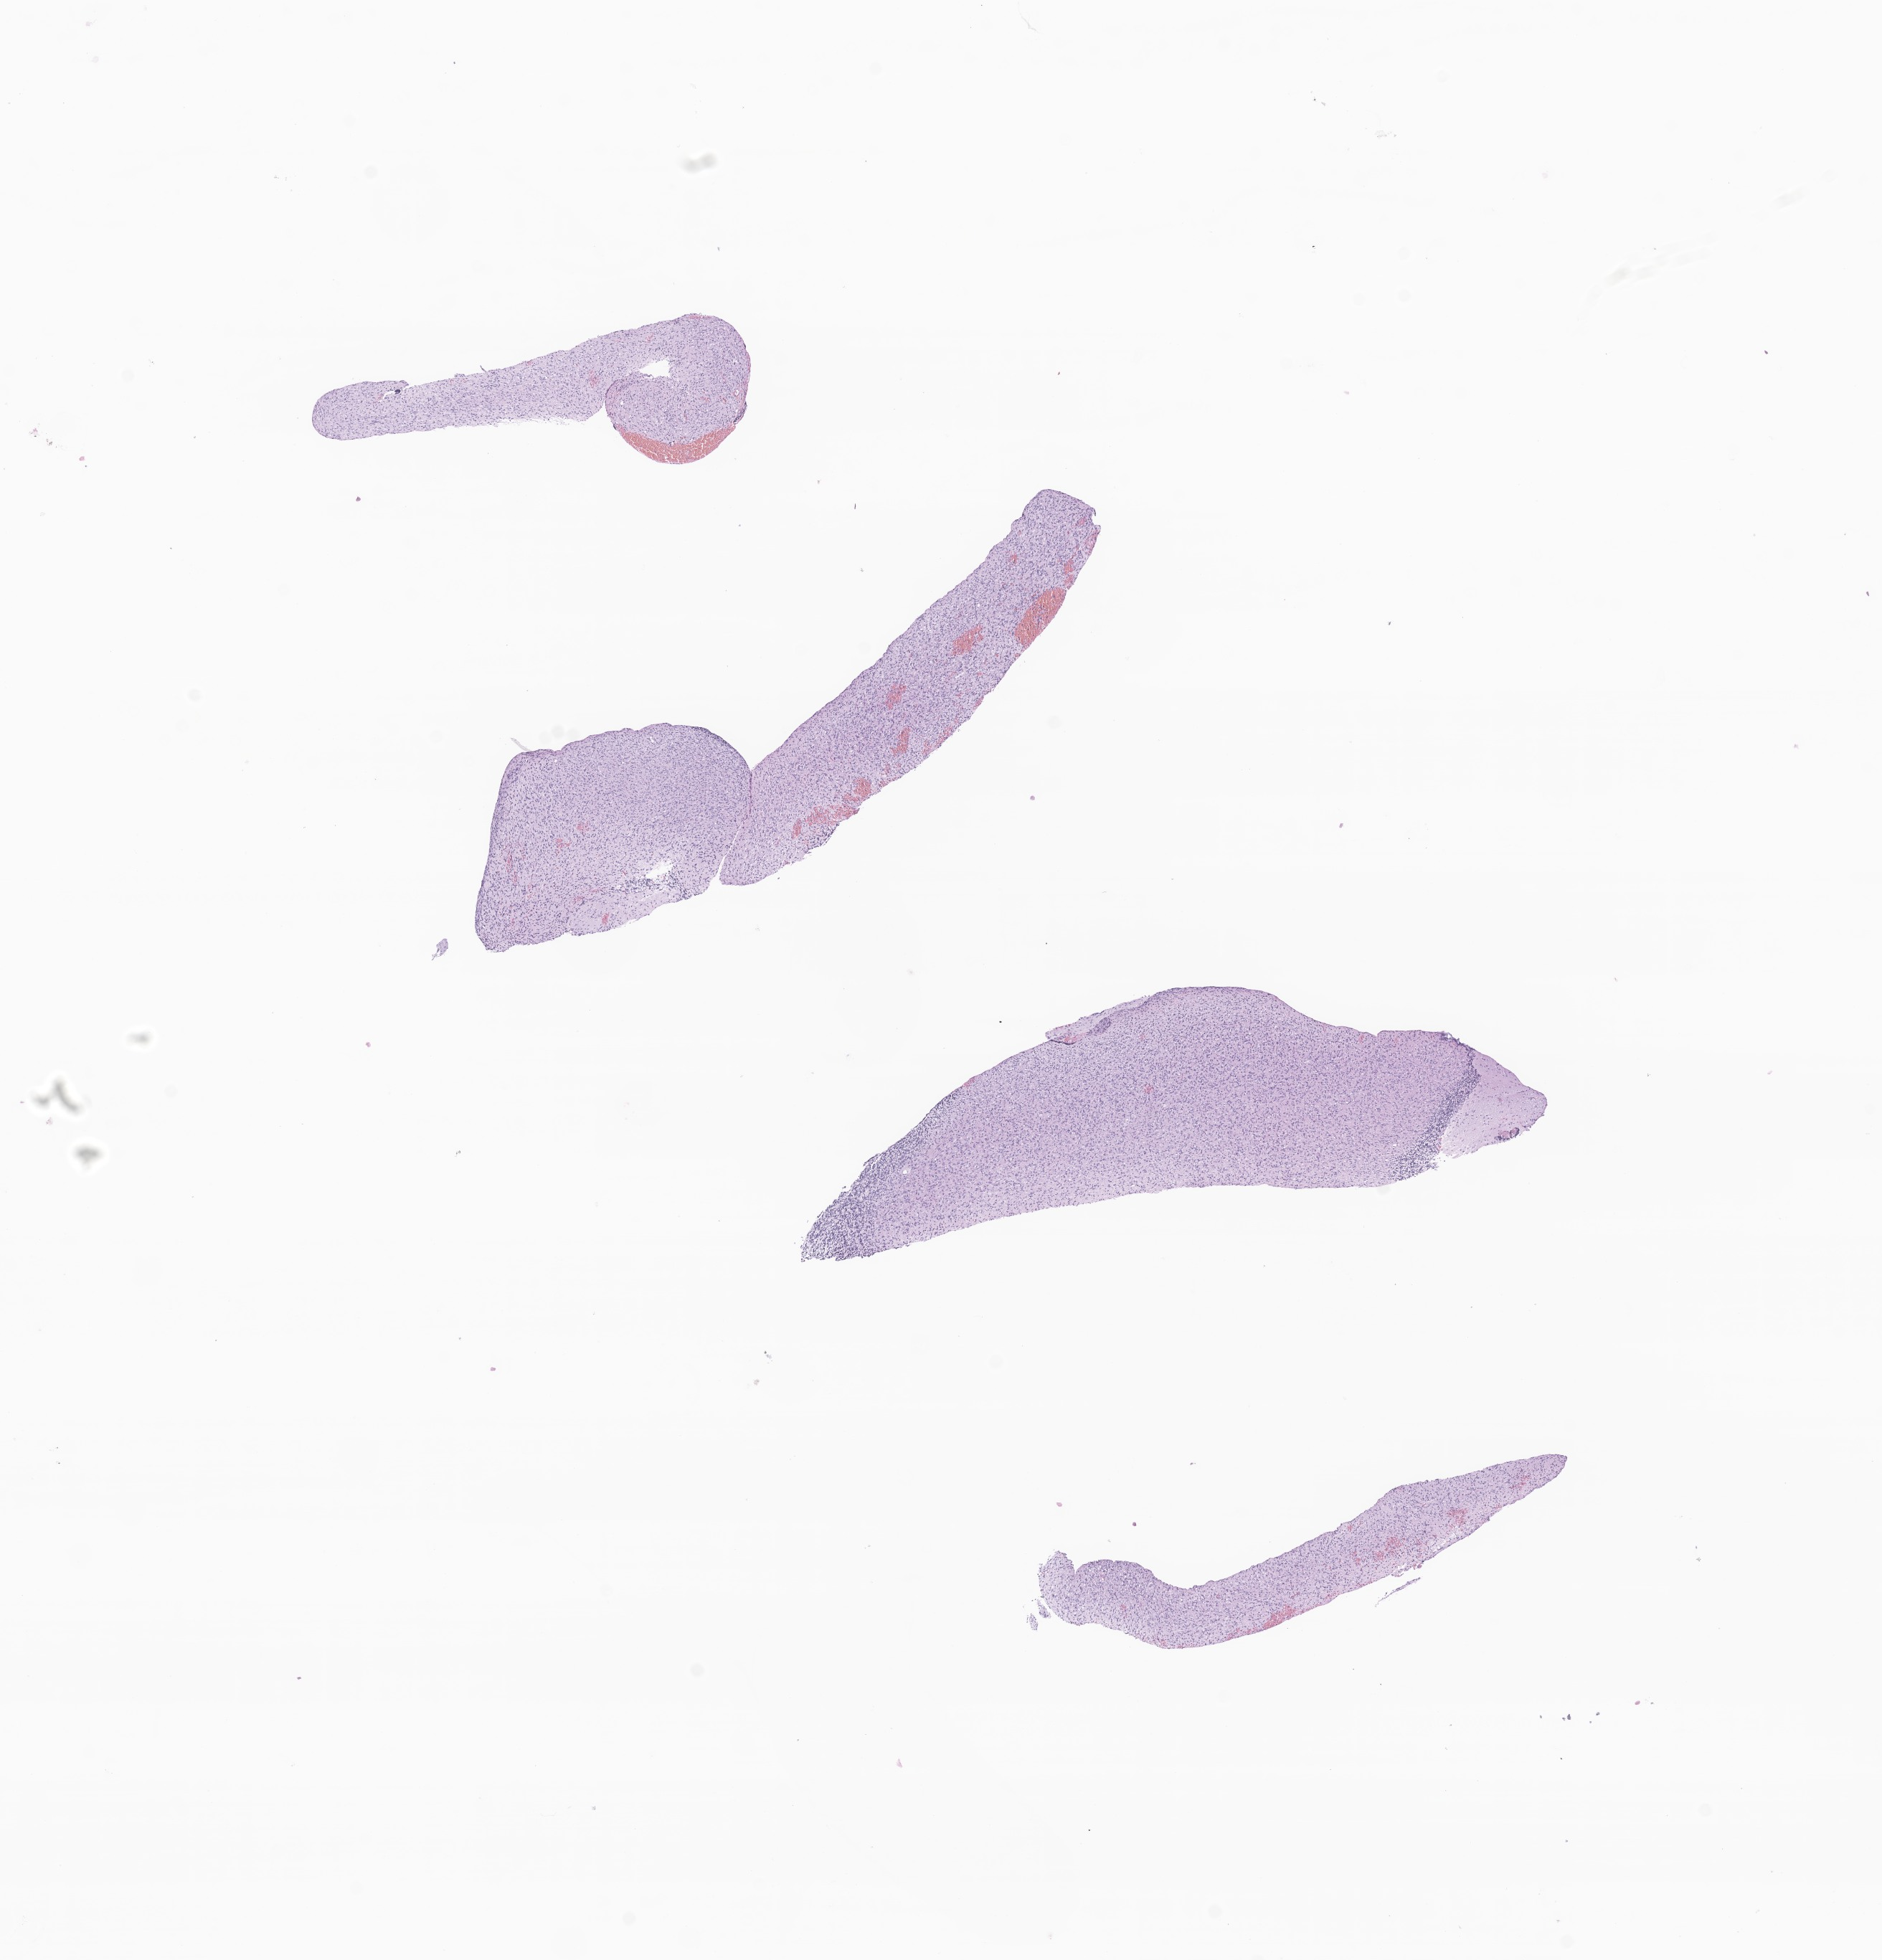
H&E whole-slide image of tumor tissue from the cerebellum — whole scanned area (about 11.1 x 11.5 mm) shown as a low-resolution overview. FFPE section. Patient female; age 38 months (3 years 2 months).
Diagnosis (ICD-O-3 morphology term): Glioma, malignant.